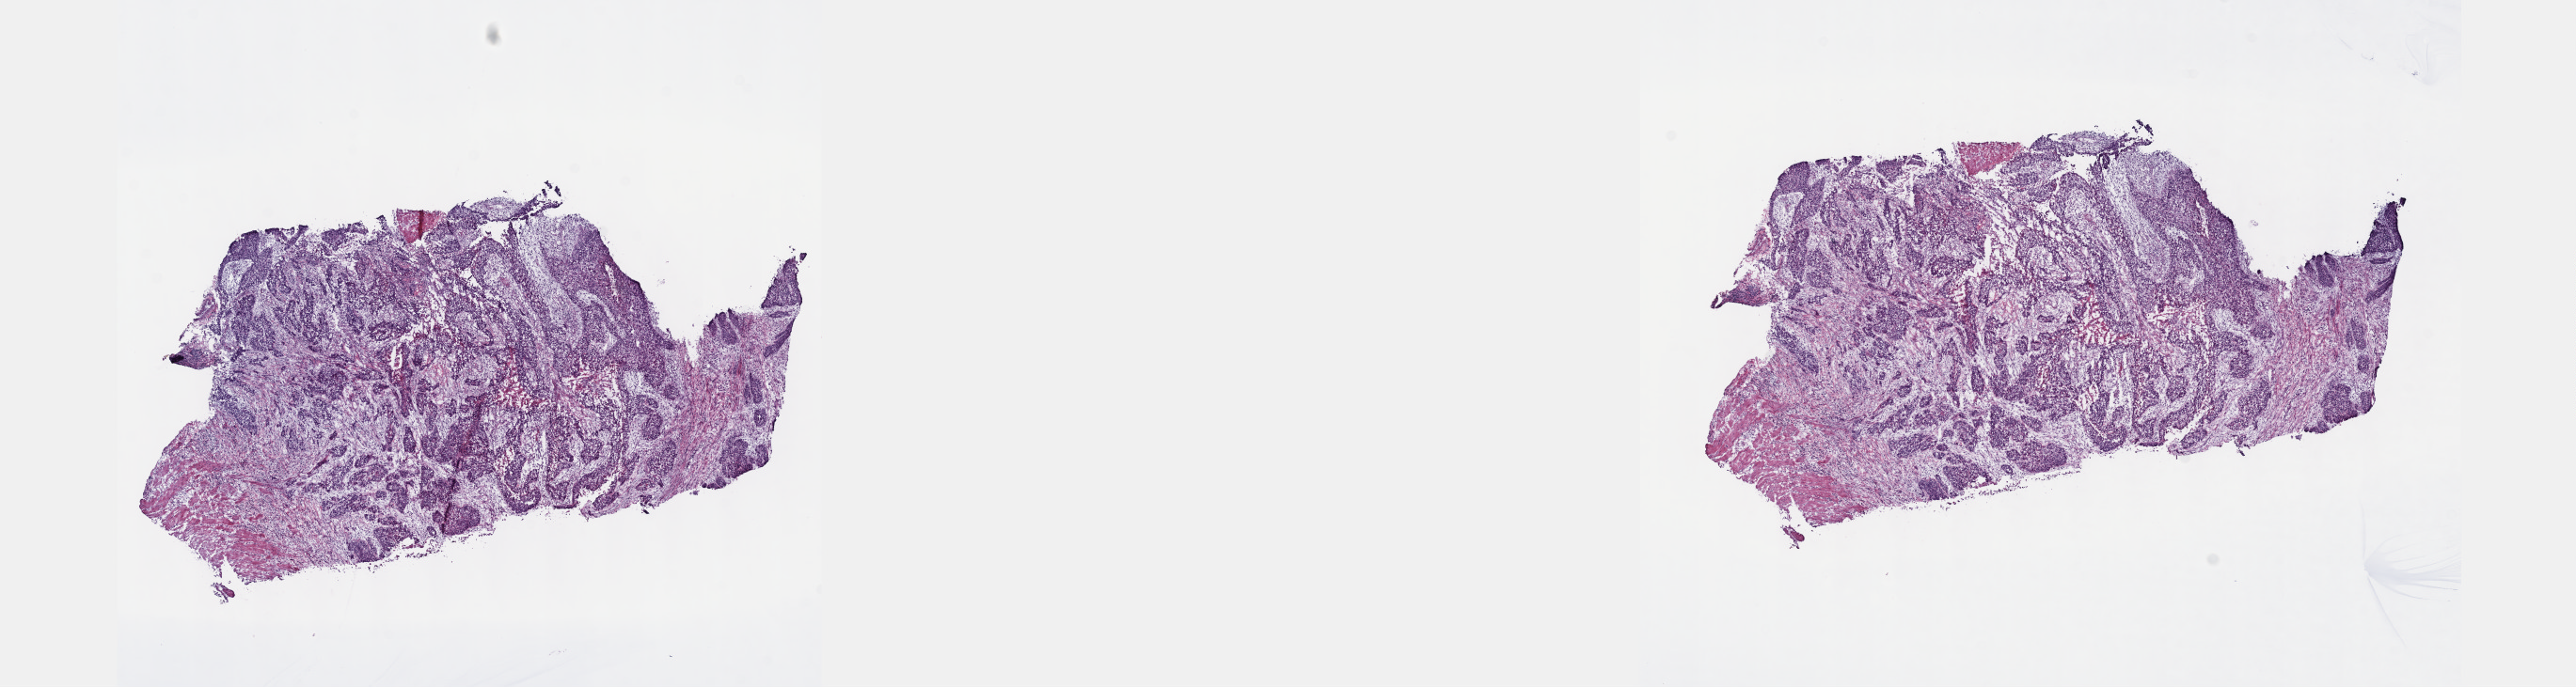
Digitized Hematoxylin and eosin (H&E) stained tissue section (whole slide) — low-resolution overview of the scanned area, about 22.1 x 5.9 mm, frozen section from the top of the tissue portion, sample: primary tumour, esophagus. Patient: female, age at initial diagnosis 65 years. Histologic grade: G2 (moderately differentiated). Pathologist review of this section (percent, as recorded): tumour cells 70%, tumour nuclei 70%, normal cells 0%, stromal cells 27%, necrosis 3%. Inflammatory infiltration, as recorded: lymphocyte infiltration 3%, monocyte infiltration 2%, neutrophil infiltration 6%.
- AJCC pathologic stage: IV (7th edition)
- pathologic diagnosis: Squamous cell carcinoma, NOS (middle third of esophagus)
- lymph nodes positive (case pathology): 9 of 27 examined
- TNM: T3 N3 M1